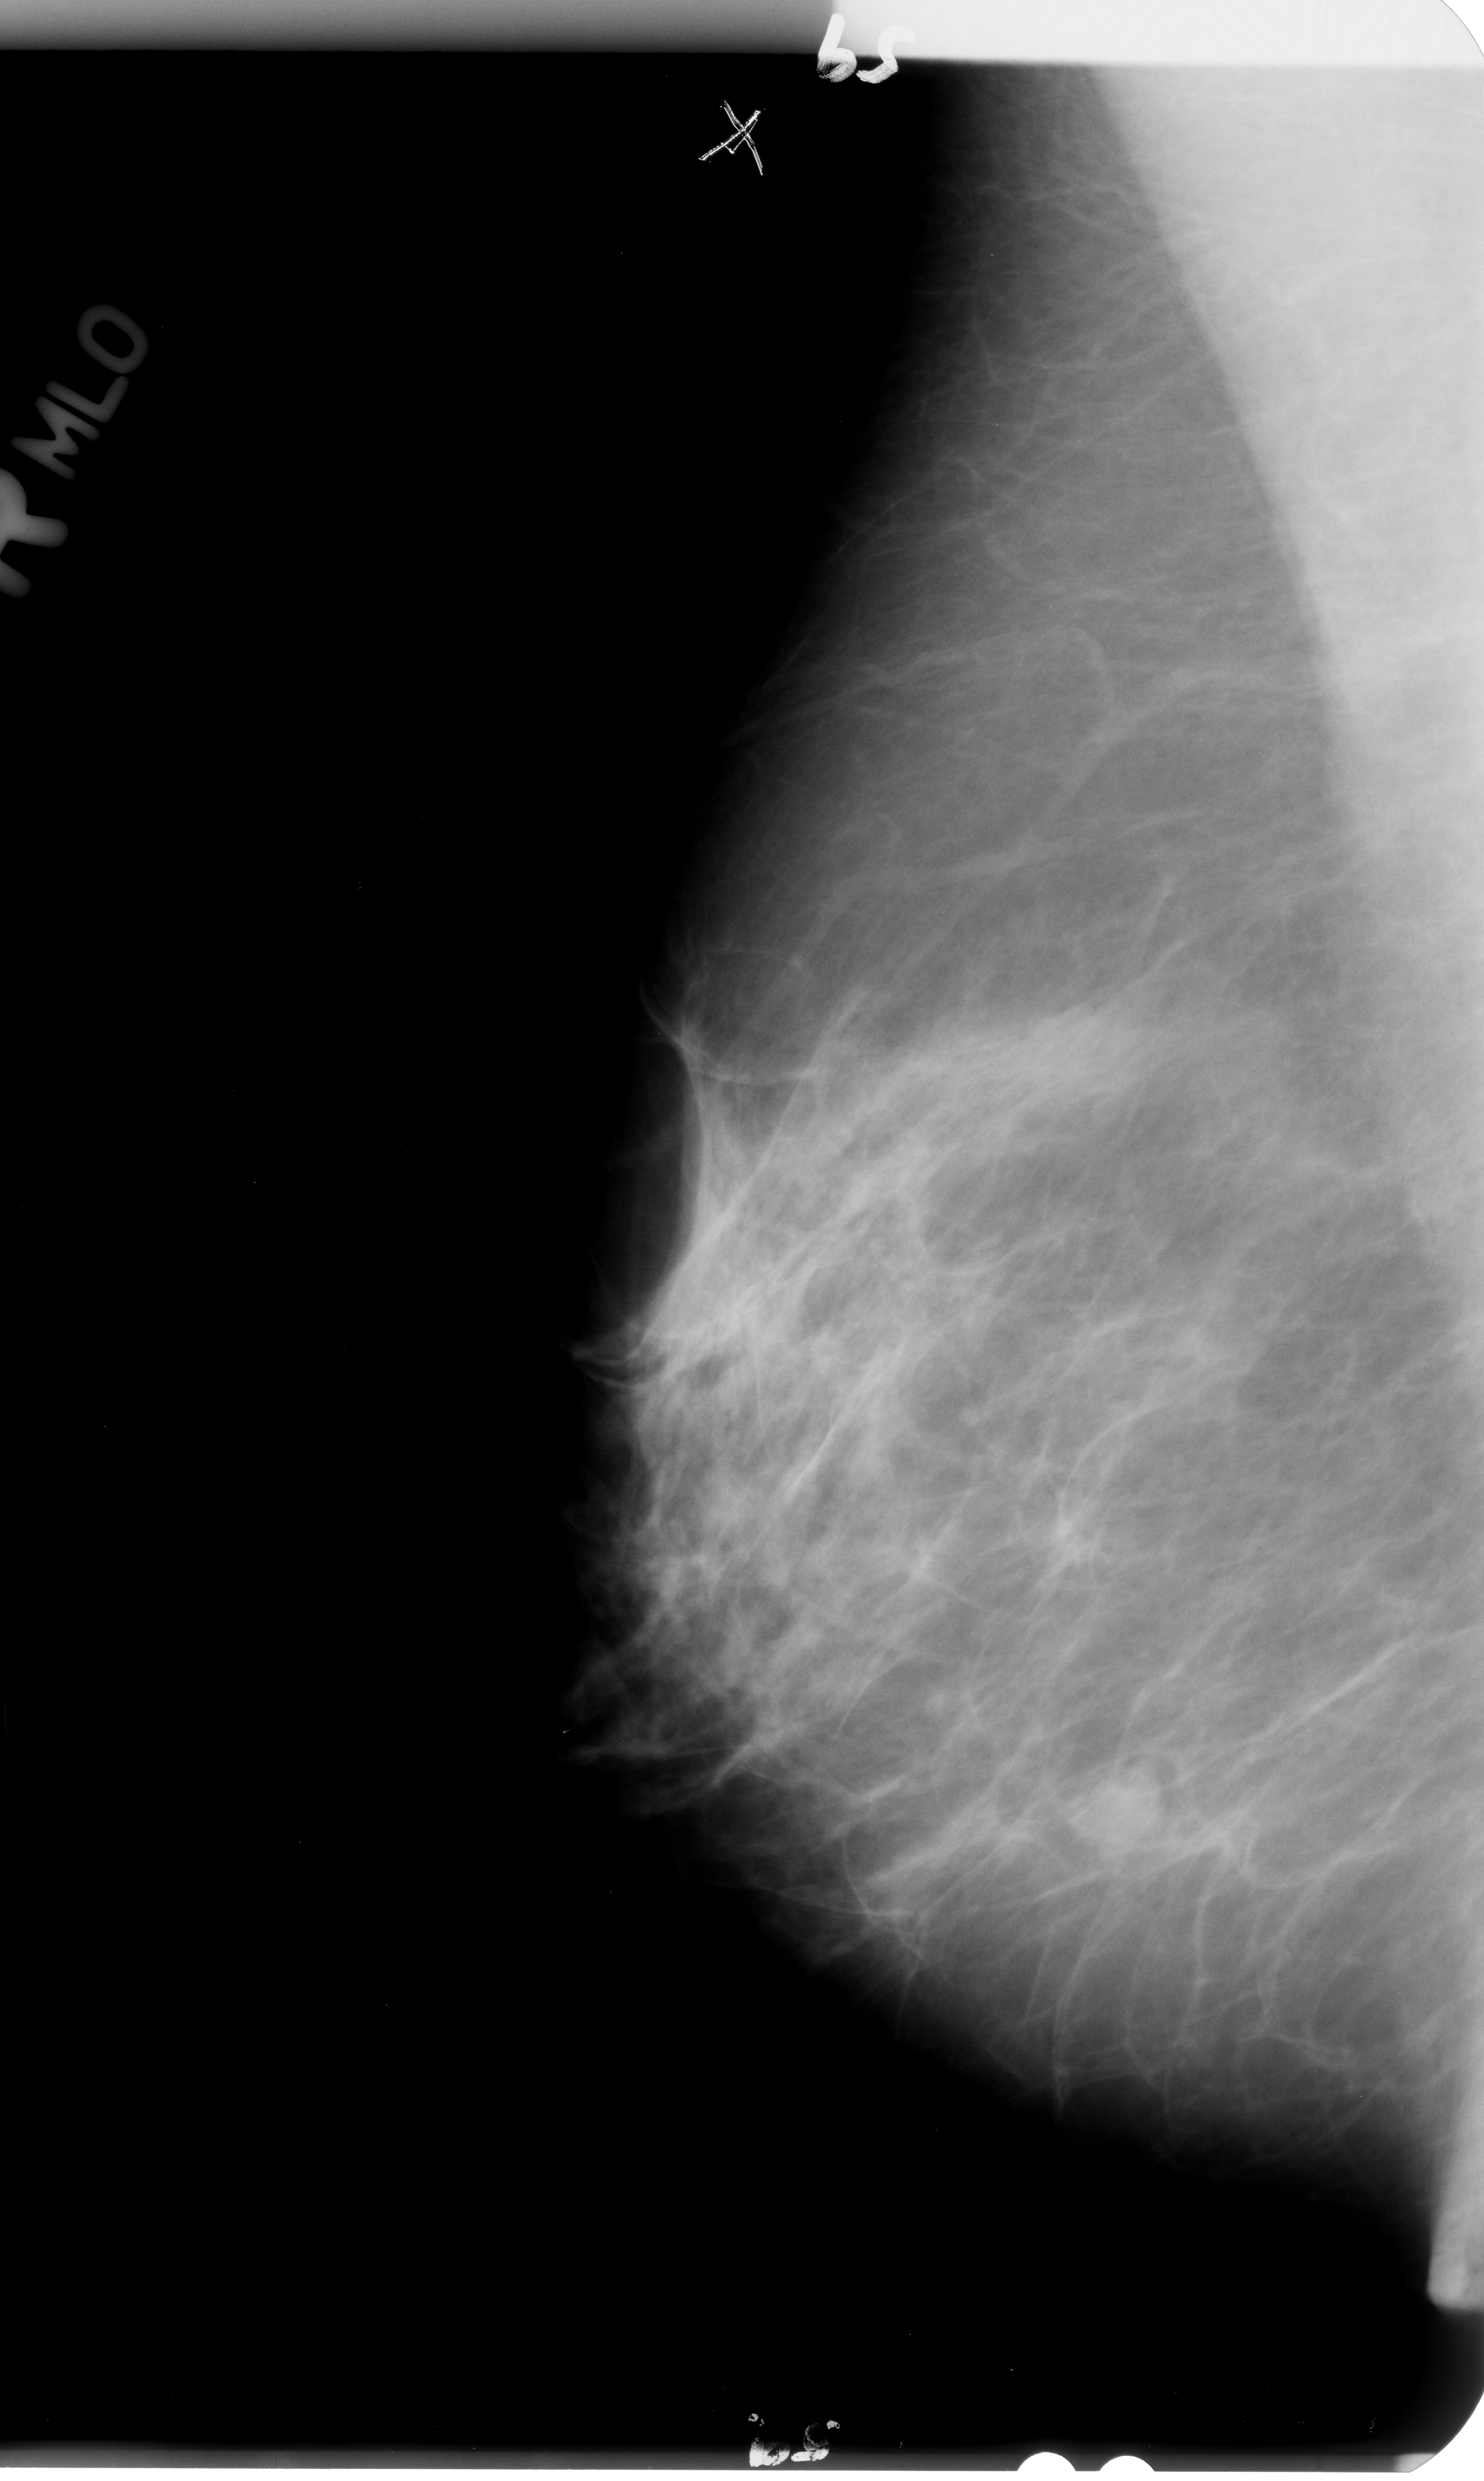
Mammogram (digitized film); right breast; mediolateral oblique (MLO) view; breast composition: scattered fibroglandular densities (BI-RADS density category 2 of 4); 1484 × 2481 image matrix.
Expert-marked regions of interest on this image (one box per marked abnormality):
- mass, shape irregular, margins microlobulated / ill defined; BI-RADS assessment category 4; pathology (as recorded): benign: bounding box (x1, y1, x2, y2) in pixels: (1055, 1746, 1163, 1875)